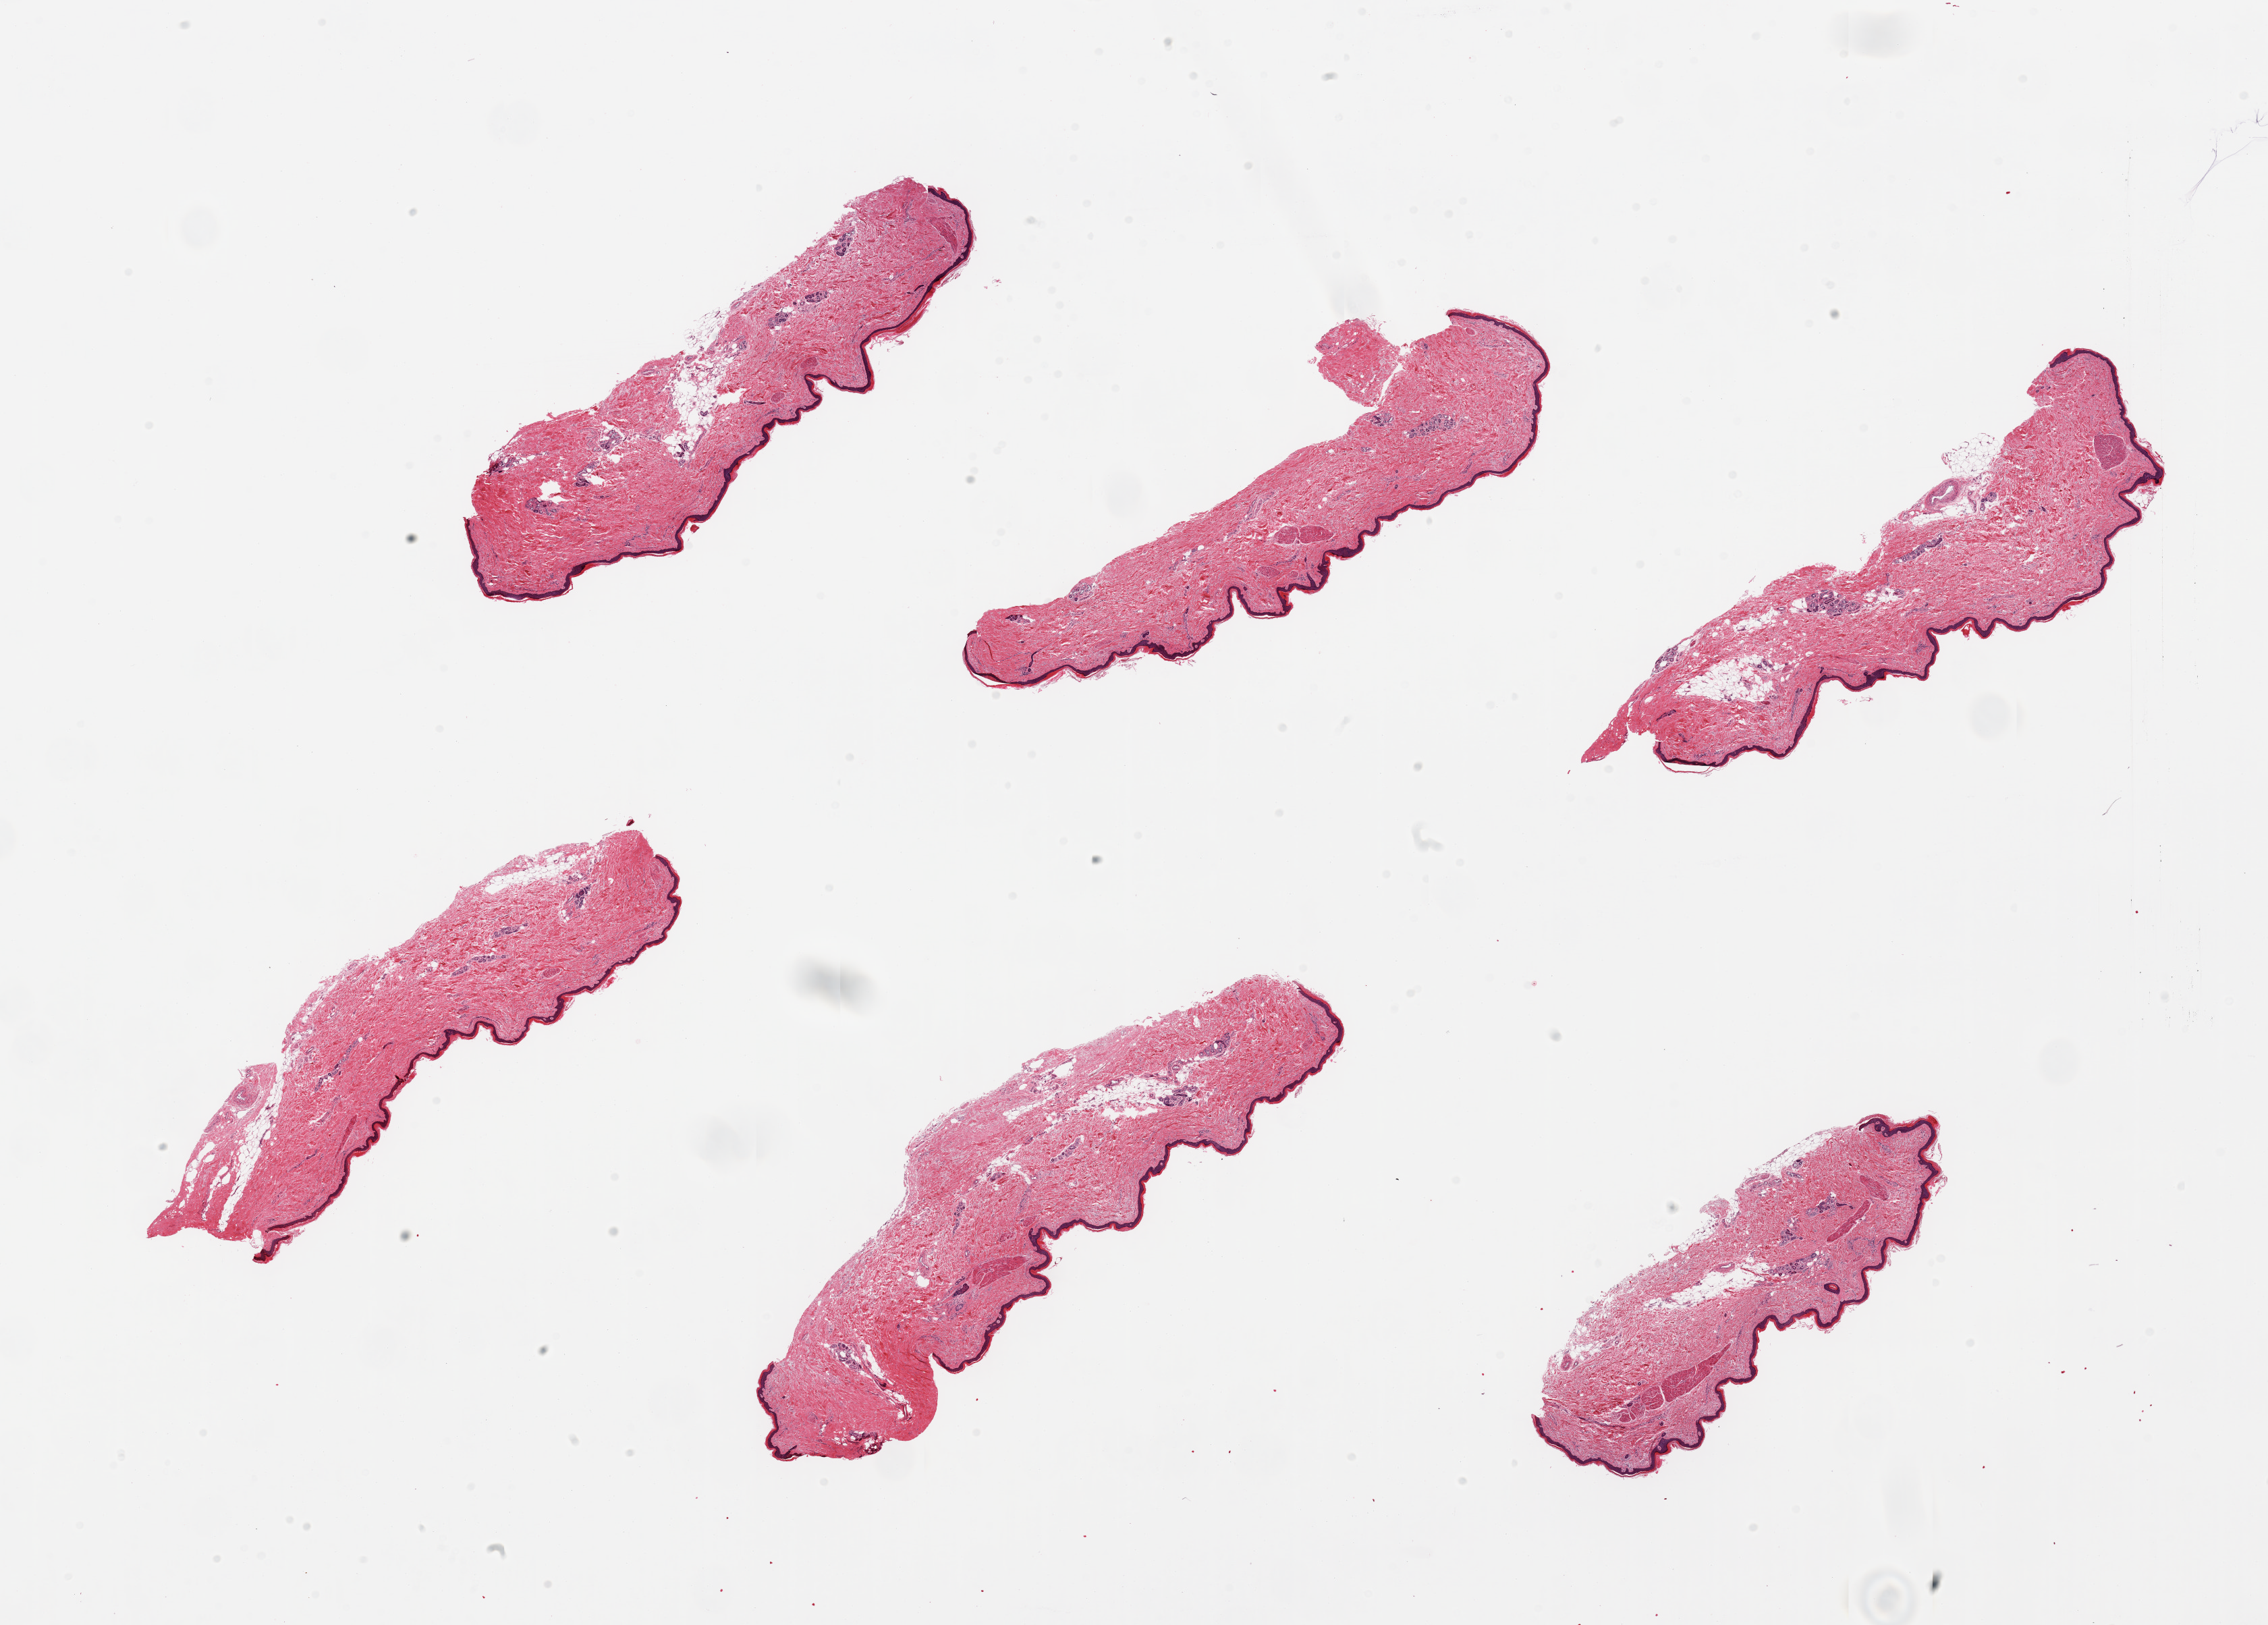
Haematoxylin and eosin whole-slide image — a low-resolution overview of the entire scanned area, about 26.6 x 19.0 mm, PAXgene-fixed, paraffin-embedded tissue, target tissue: skin of lower leg, tissue donor sample.
Pathologist's review note for this sample: 6 pieces; well trimmed; 5-10% dermal fat.